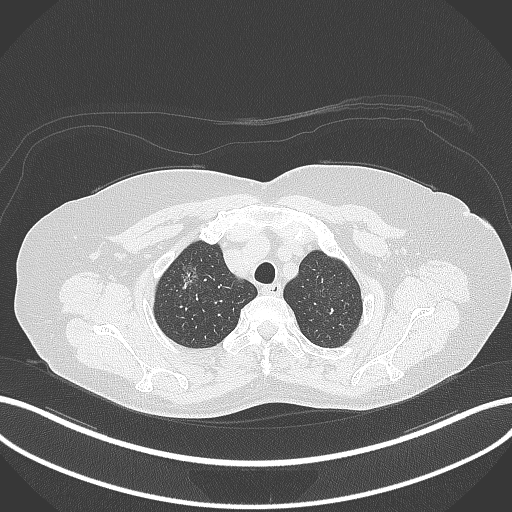
Chest CT, one axial slice; position 300 of 365 along the scan axis; reconstruction kernel B70f; 120 kVp; lung window (W 1500 / L -600 HU); 1 mm slice thickness; 512 × 512 image matrix. Female patient, age 62 years. Case-level facts recorded for this patient, not image findings: clinical TNM (as recorded): T1c N0 M0.
Annotated regions visible in this slice (rectangle marked by the reading radiologist):
- lung tumour (recorded histology: adenocarcinoma): bounding box [x1, y1, x2, y2] px = [176, 258, 209, 296]